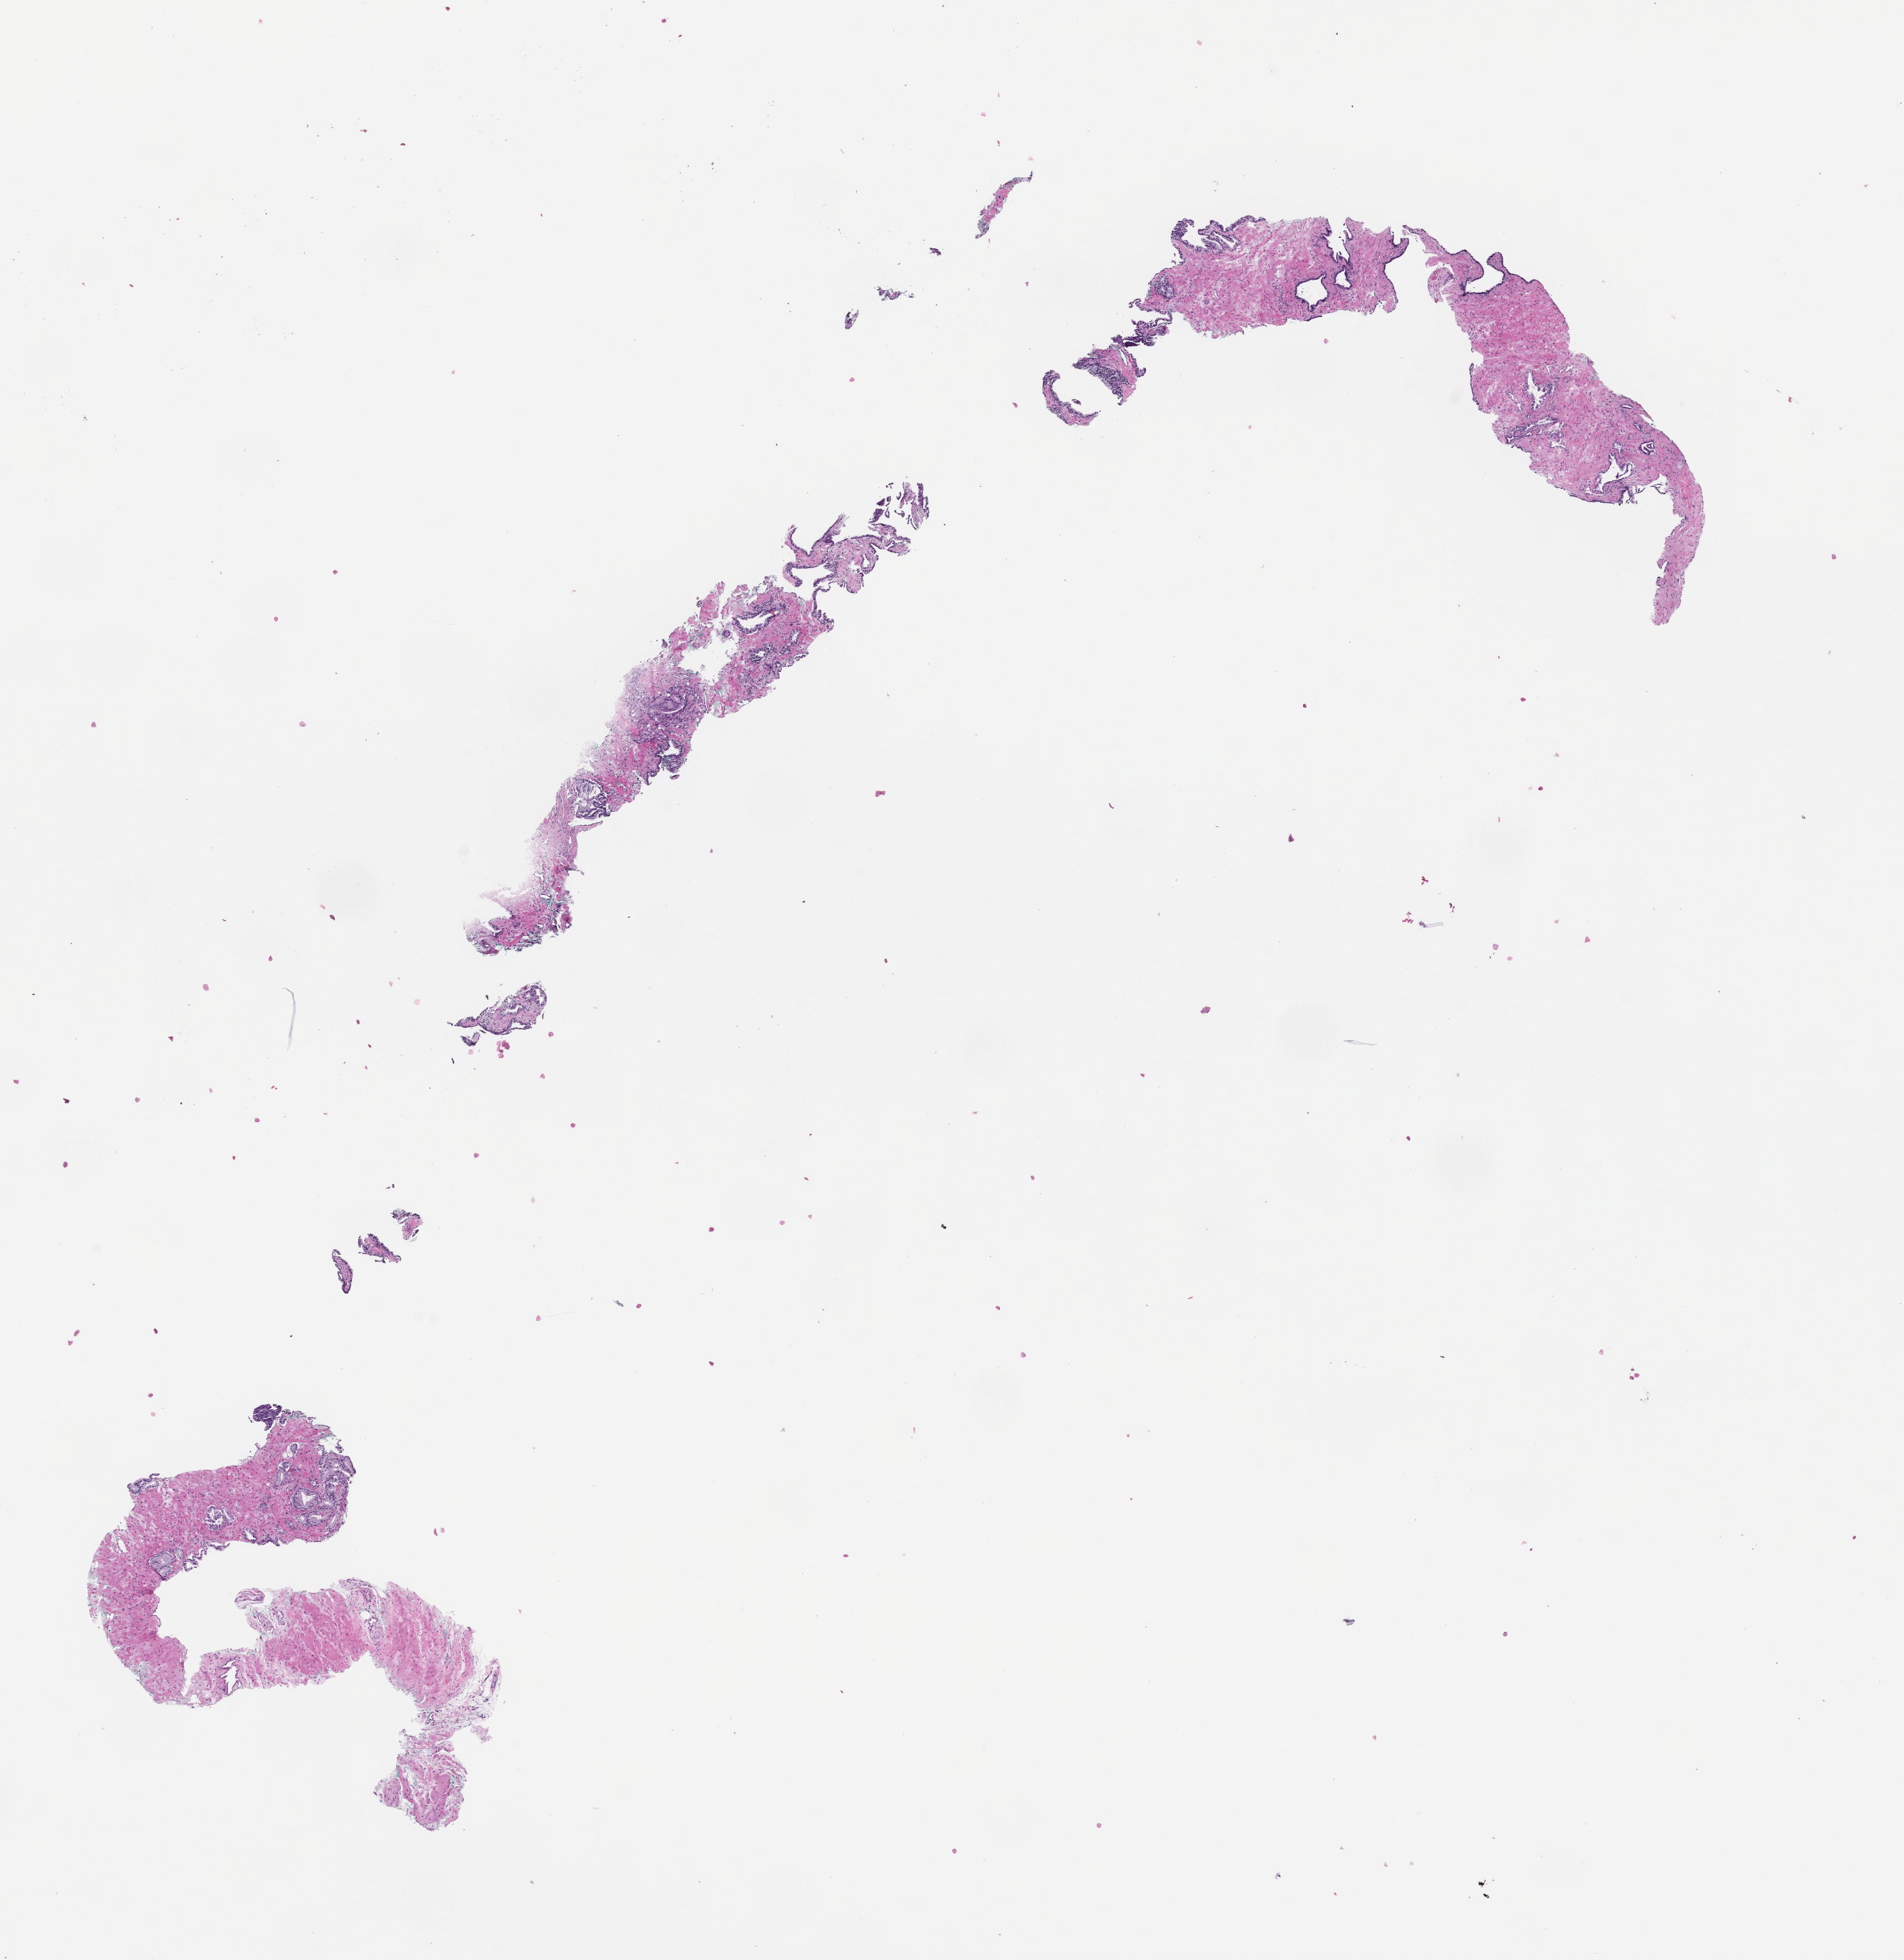
Hematoxylin and eosin (H&E) whole-slide image, low-resolution overview of the scanned area, about 11.1 x 11.4 mm, FFPE section, tissue site: prostate. Male patient.
• this section: primary tumor
• diagnosis: Prostate Carcinoma